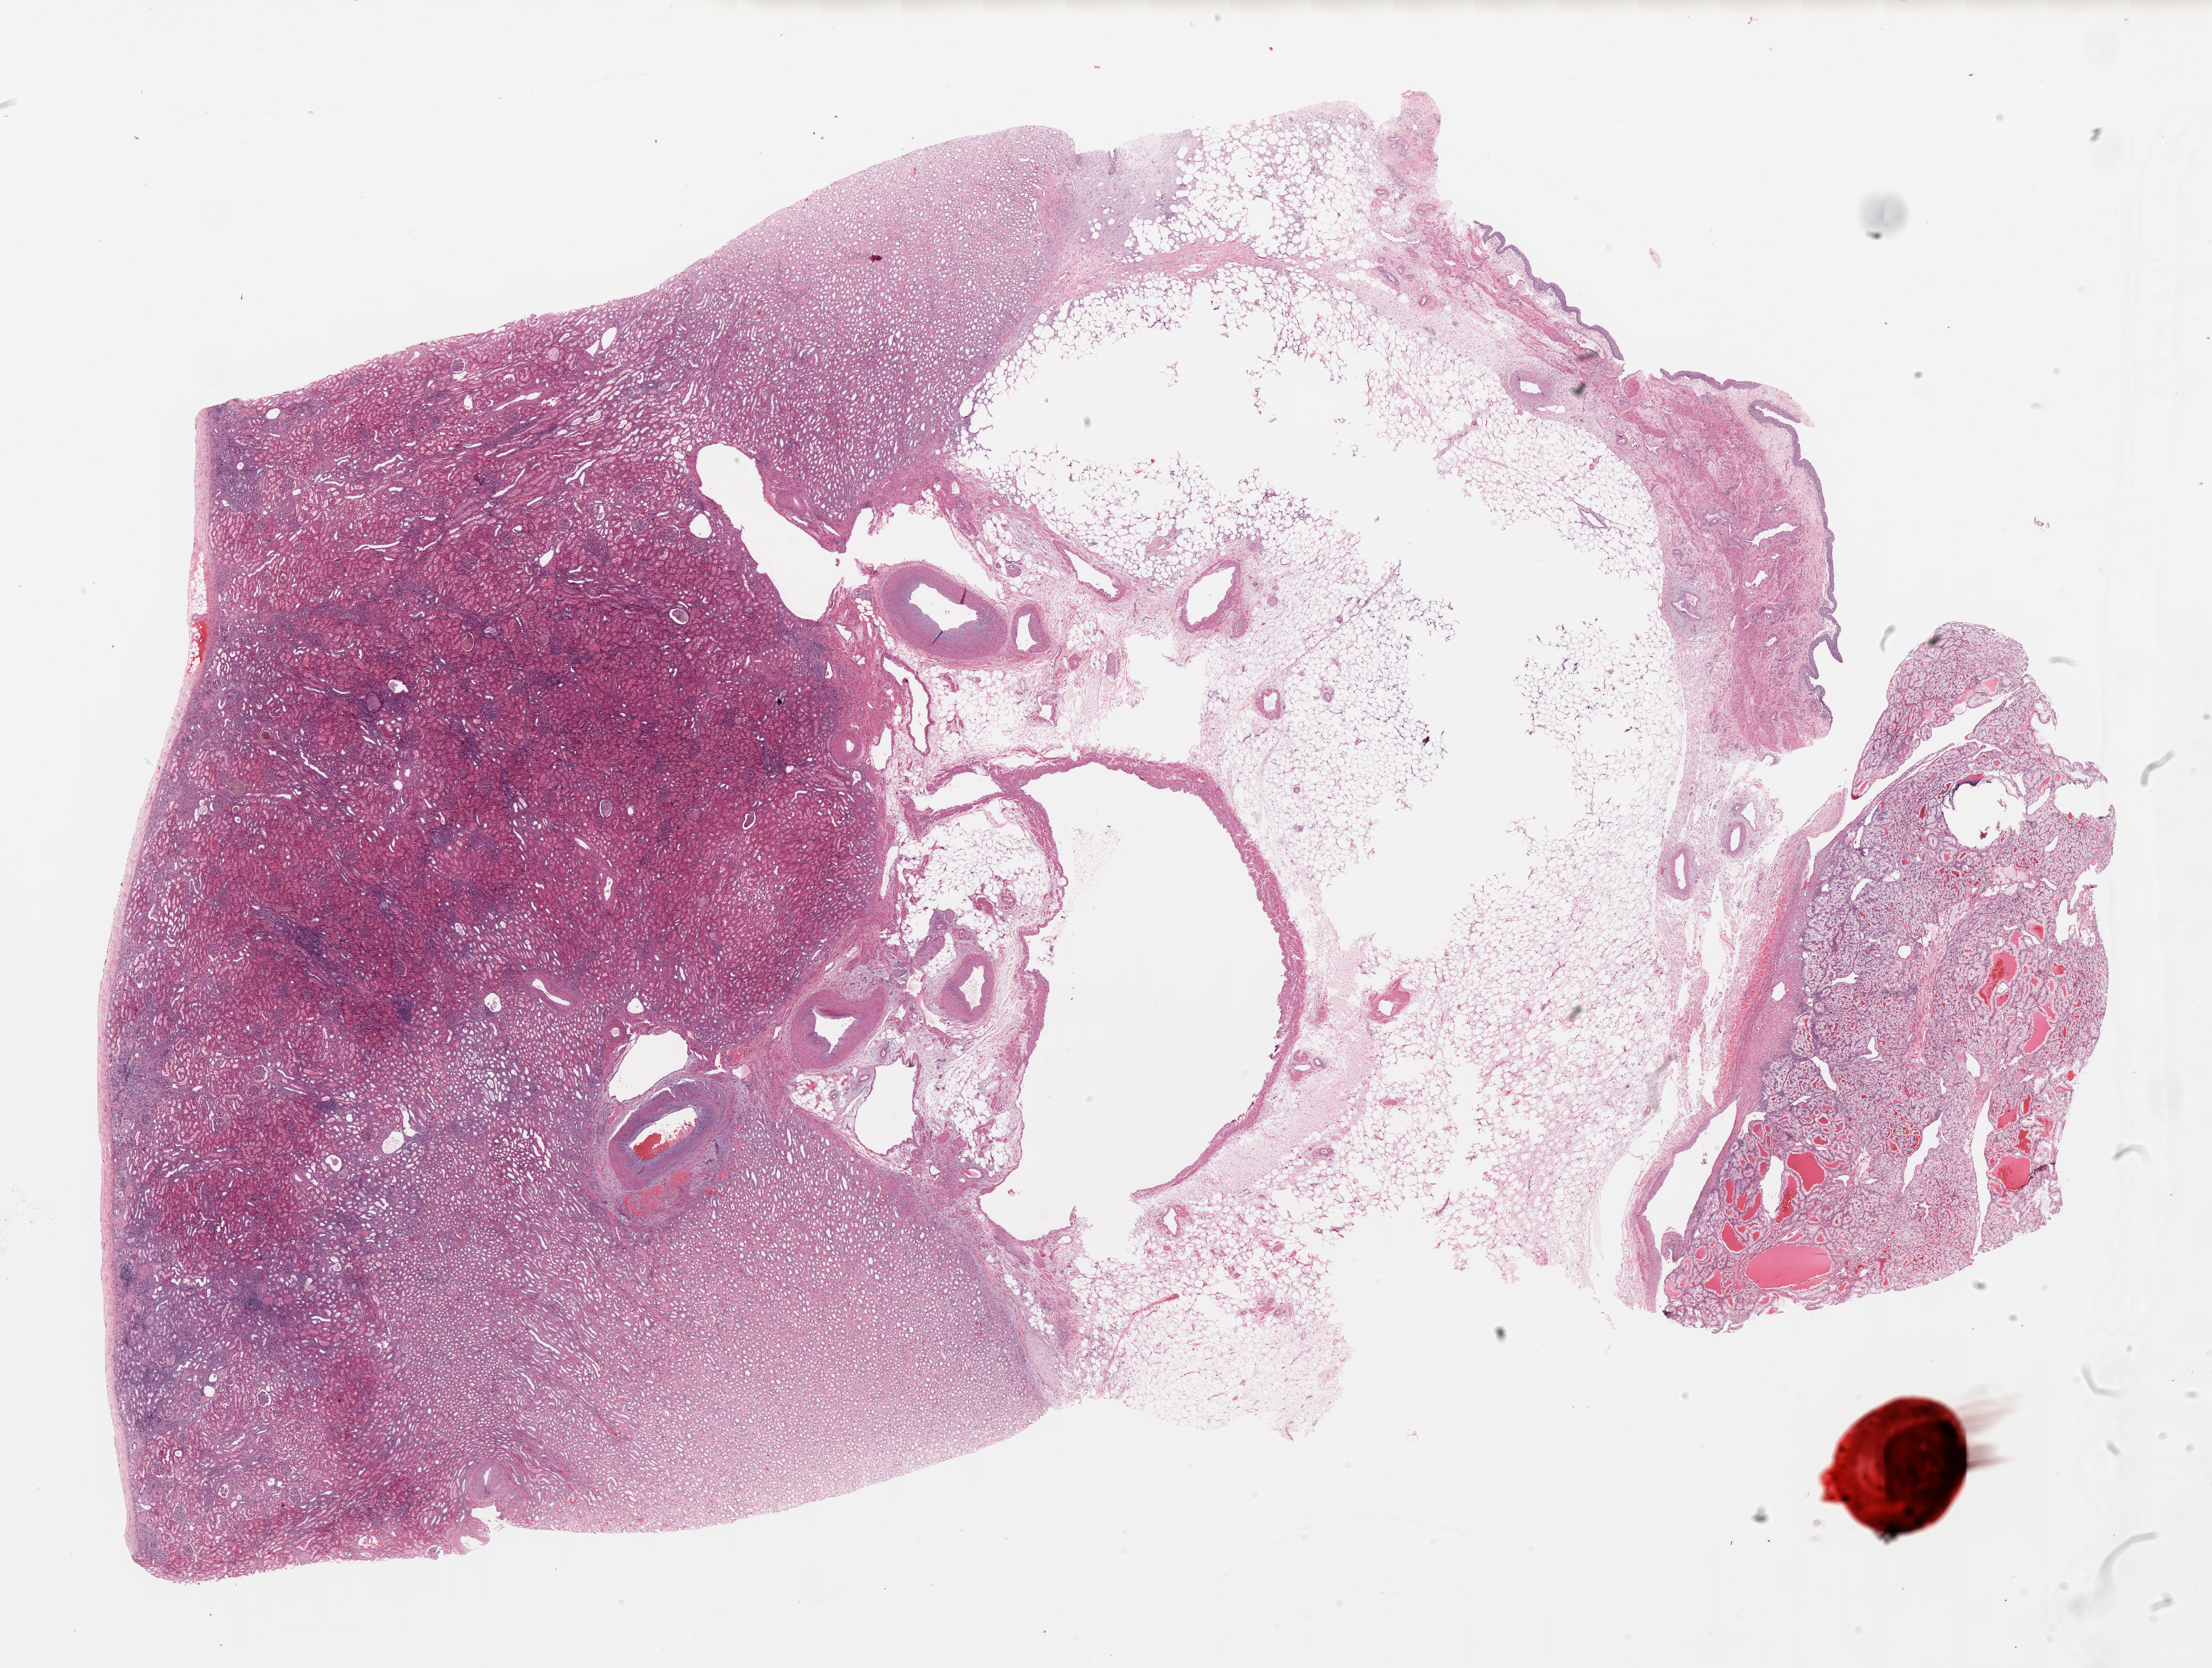
Whole-slide histology image, H&E-stained, shown as a low-resolution overview of the whole scanned area (about 27.1 x 20.4 mm); formalin-fixed paraffin-embedded (FFPE) diagnostic section; primary tumour sample from the kidney. Female, age 70 years at initial diagnosis. Histologic grade: G2 (moderately differentiated).
• AJCC pathologic stage: I
• laterality: left
• diagnosis: Clear cell adenocarcinoma, NOS